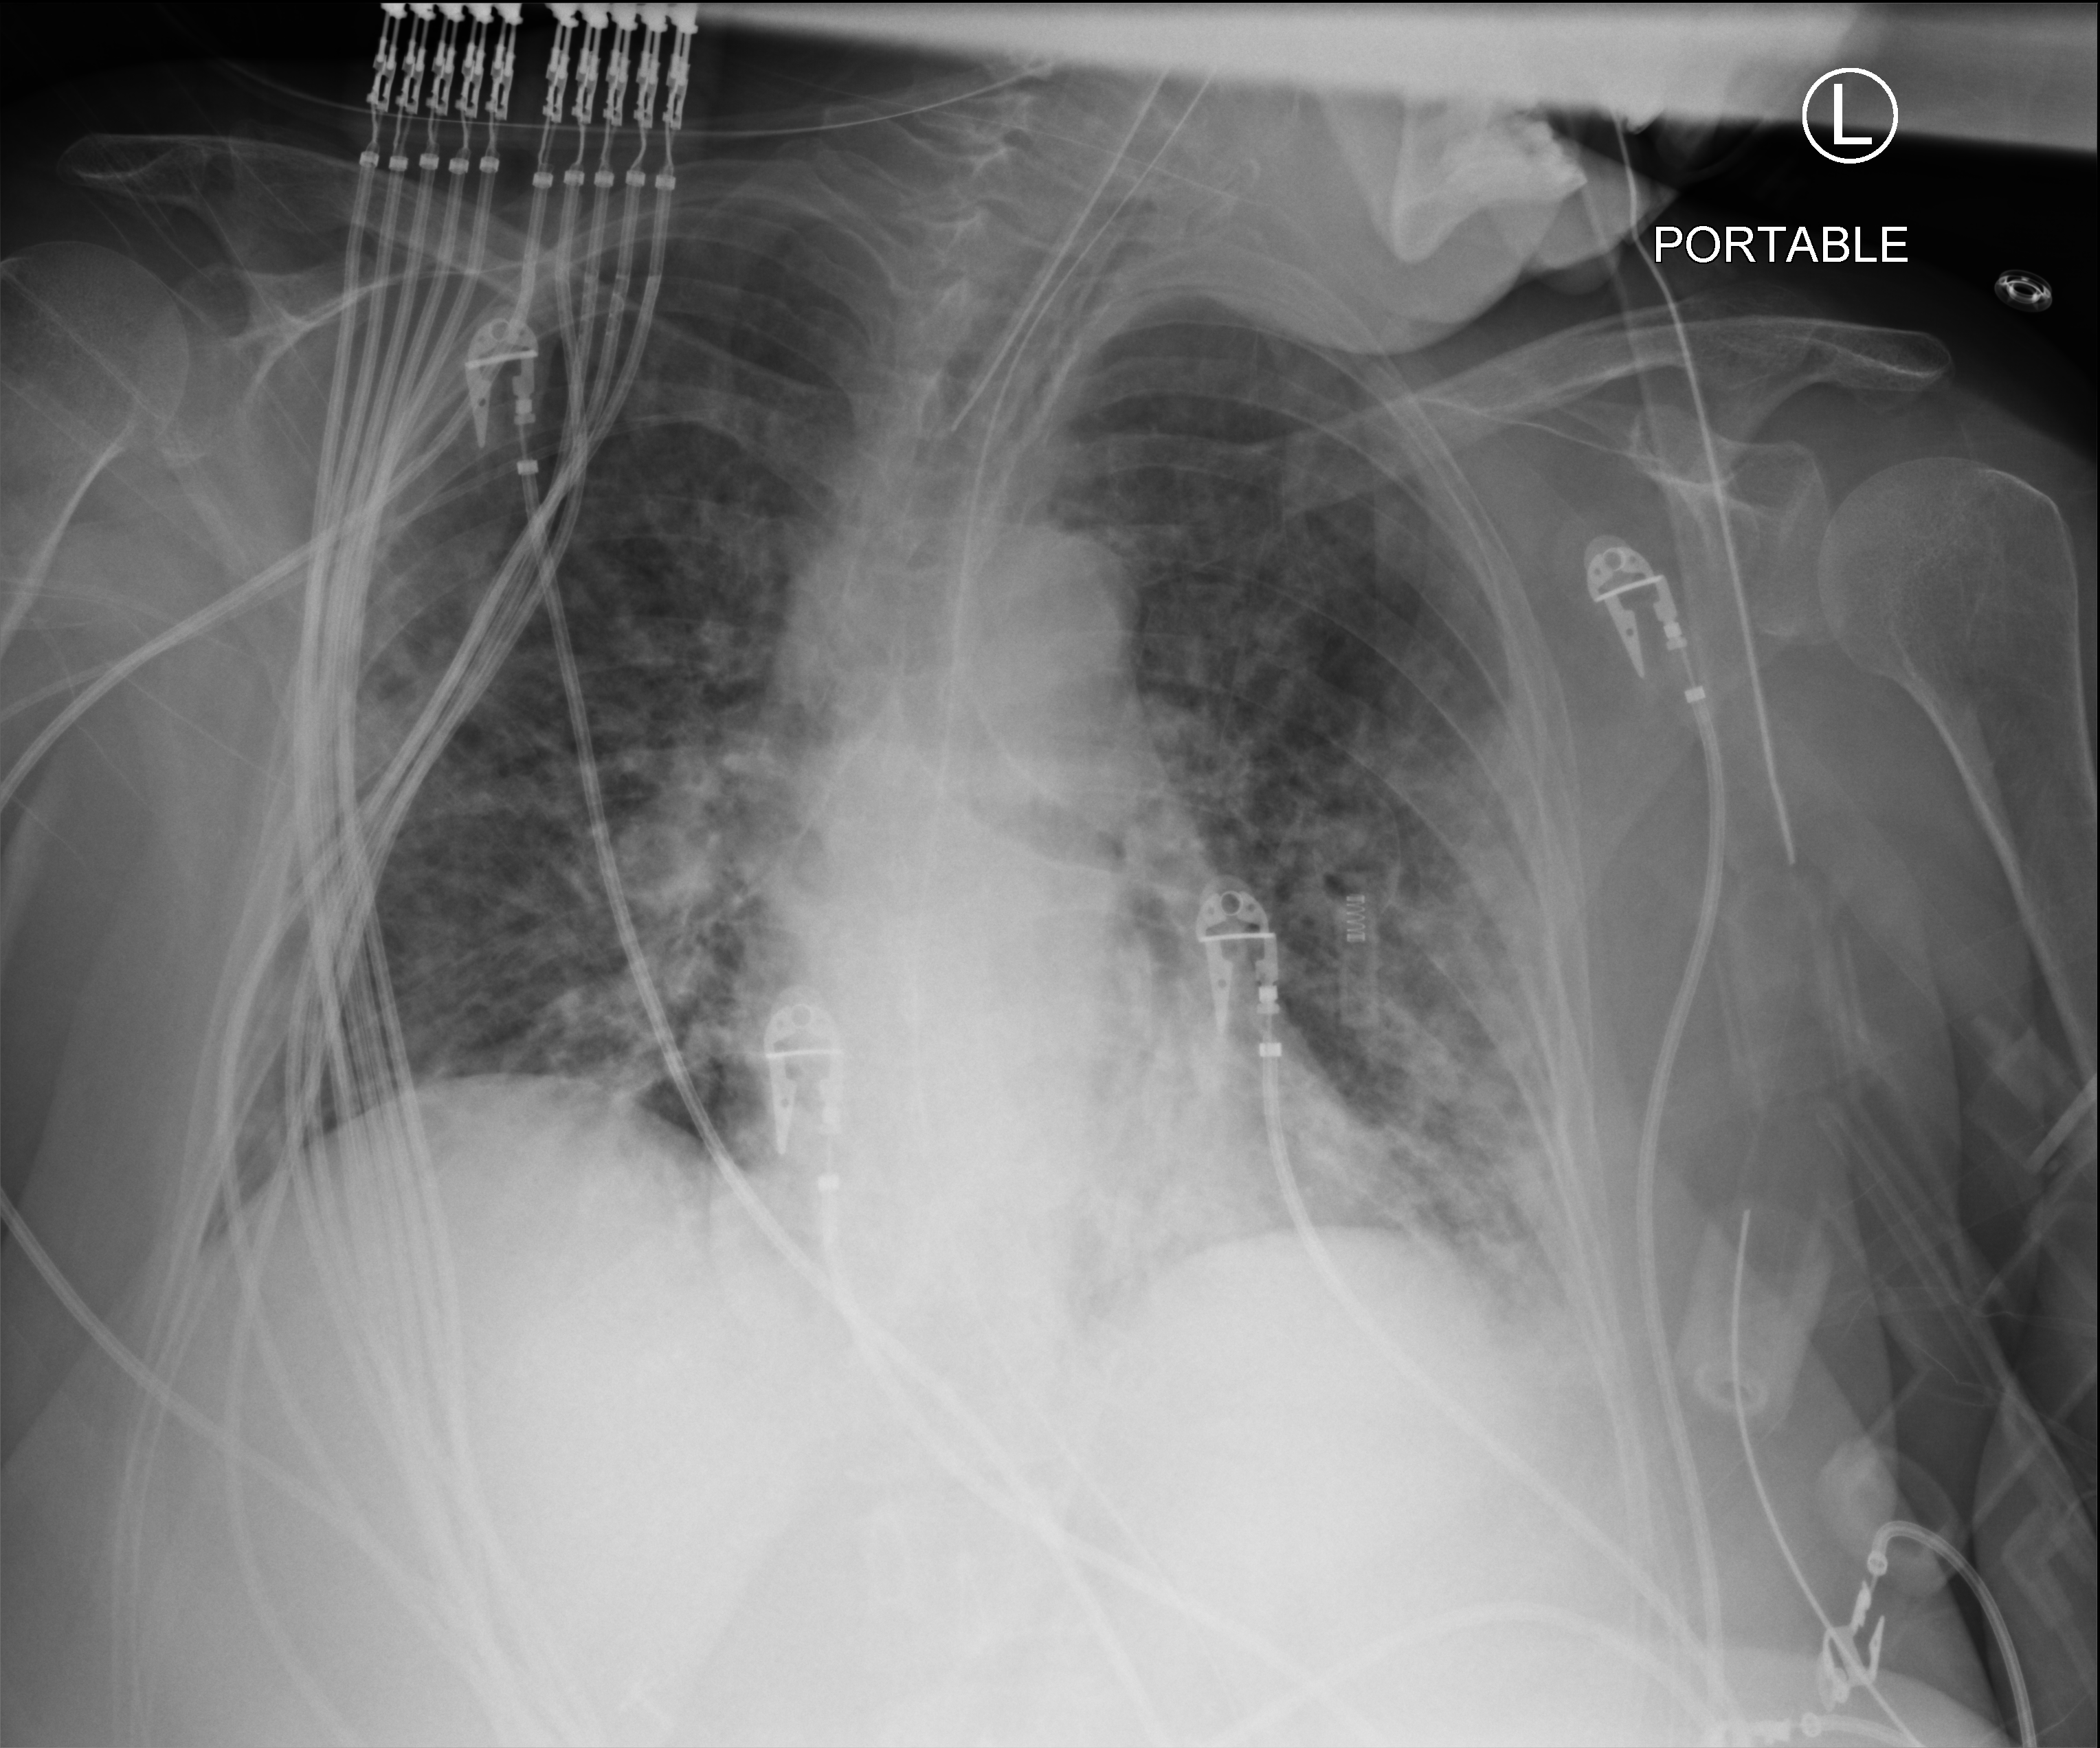
Chest X-ray (portable); anteroposterior (AP) projection. Female patient hospitalised with COVID-19, age 18–59 years.
Hospital-stay facts (about this admission, not read from this image; timing relative to this image not recorded): length of hospital stay: 22 days; smoking status (admission record): never; admitted to intensive care during this hospital stay: yes.